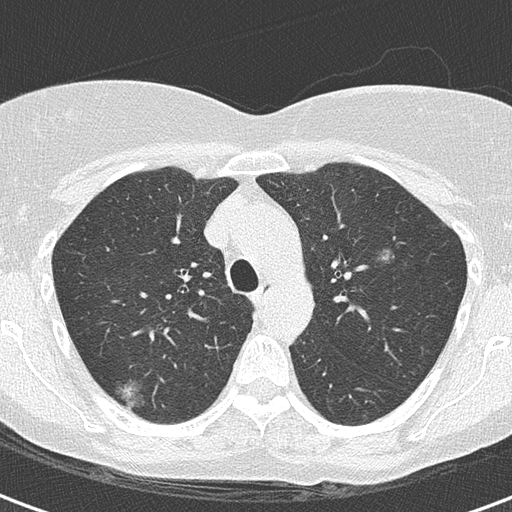
Low-dose screening chest CT, axial slice, second annual screen, lung window (W 1500 / L -600 HU), lung (sharp) reconstruction kernel (B50f), 120 kVp, slice 47 of 172 in the series. Female, age 56 years at enrolment. Current smoker at enrolment.
- Lesion marked by an expert reader, bounding box (x1, y1, x2, y2) in pixels: (90, 367, 153, 419).
- Screening reader's record for this exam (one nodule recorded; not confirmed to be the boxed lesion): non-calcified nodule or mass ≥4 mm, right upper lobe, 18 × 18 mm, mixed attenuation, pre-existing on the prior screen: yes.
- Lung cancer was diagnosed 93 days after this screen: bronchiolo-alveolar adenocarcinoma, NOS, right upper lobe, well differentiated (G1), stage IA (AJCC 6th edition), 15 mm at pathology.